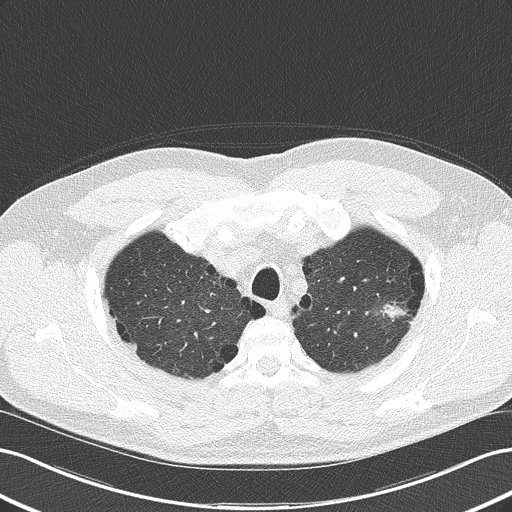
Axial slice from a low-dose chest CT screening exam; second annual screen; lung window (W 1500 / L -600 HU); lung (sharp) reconstruction kernel (B50f); slice 38 of 177 in the series; 512 × 512 image matrix. Male participant, aged 62 years at enrolment.
Lesion marked by an expert reader, bounding box <356,285,421,341> (left, top, right, bottom; pixels). The screening reader recorded 2 non-calcified nodules or masses ≥4 mm on this exam (left upper lobe, right middle lobe); which of them this box marks is not recorded. Official screen result: positive, other. Later outcome: lung cancer diagnosed 46 days after this screen — adenocarcinoma, NOS, left upper lobe, well differentiated (G1), stage IB (AJCC 6th edition), 17 mm at pathology.